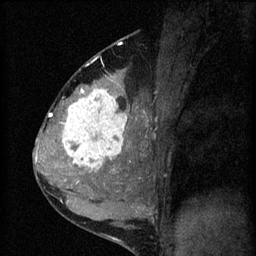
Breast MRI (dynamic contrast-enhanced), one sagittal slice; slice 34 of 60 in the series (ordered by position); 3 images stored at this slice position (order not interpretable as contrast timing); 1.5 T; TE 4.2 ms, TR 8.2 ms; 2 mm slice thickness; 256 × 256 image matrix. Female patient, age 37 years.
Structures marked on this image (semi-automatically segmented with operator editing):
- analysis volume of interest (the breast-tissue region the enhancement analysis was run in; not a lesion): bounding box [x1, y1, x2, y2] px = [53, 78, 140, 181]
- tumour enhancement mask (voxels above the 70 % enhancement threshold inside the analysis volume of interest): [62, 90, 127, 171]